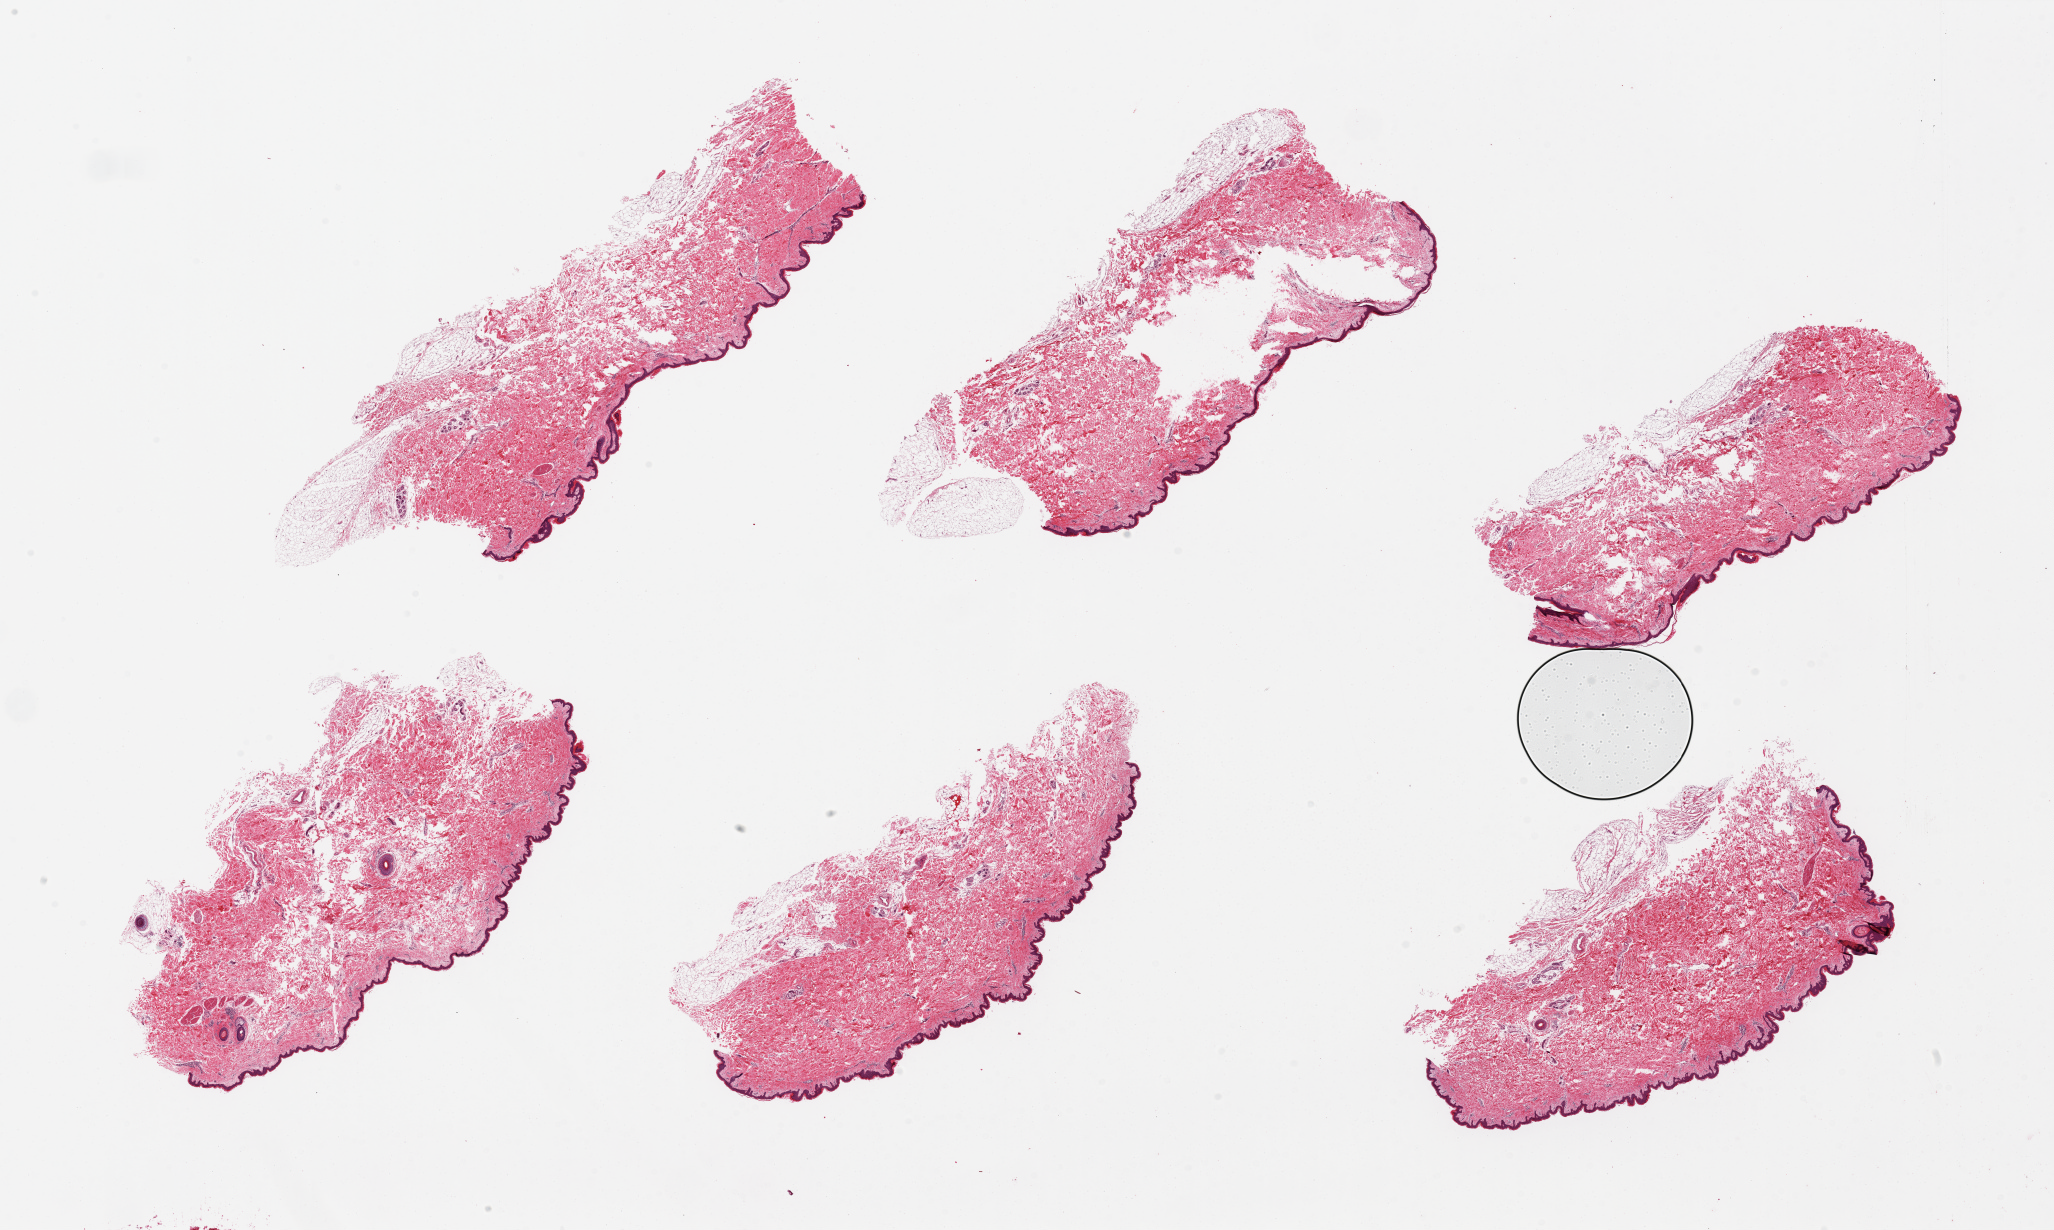
Whole-slide image, haematoxylin and eosin stain — whole scanned area (about 32.5 x 19.5 mm) shown as a low-resolution overview. PAXgene-fixed paraffin-embedded (PFPE) section. Sampled site (target tissue): skin of suprapubic region. Donor tissue sample. Donor sex: male.
Review note (as recorded): 6 pieces, all with small amounts of attached adipose tissue, up to 10%.